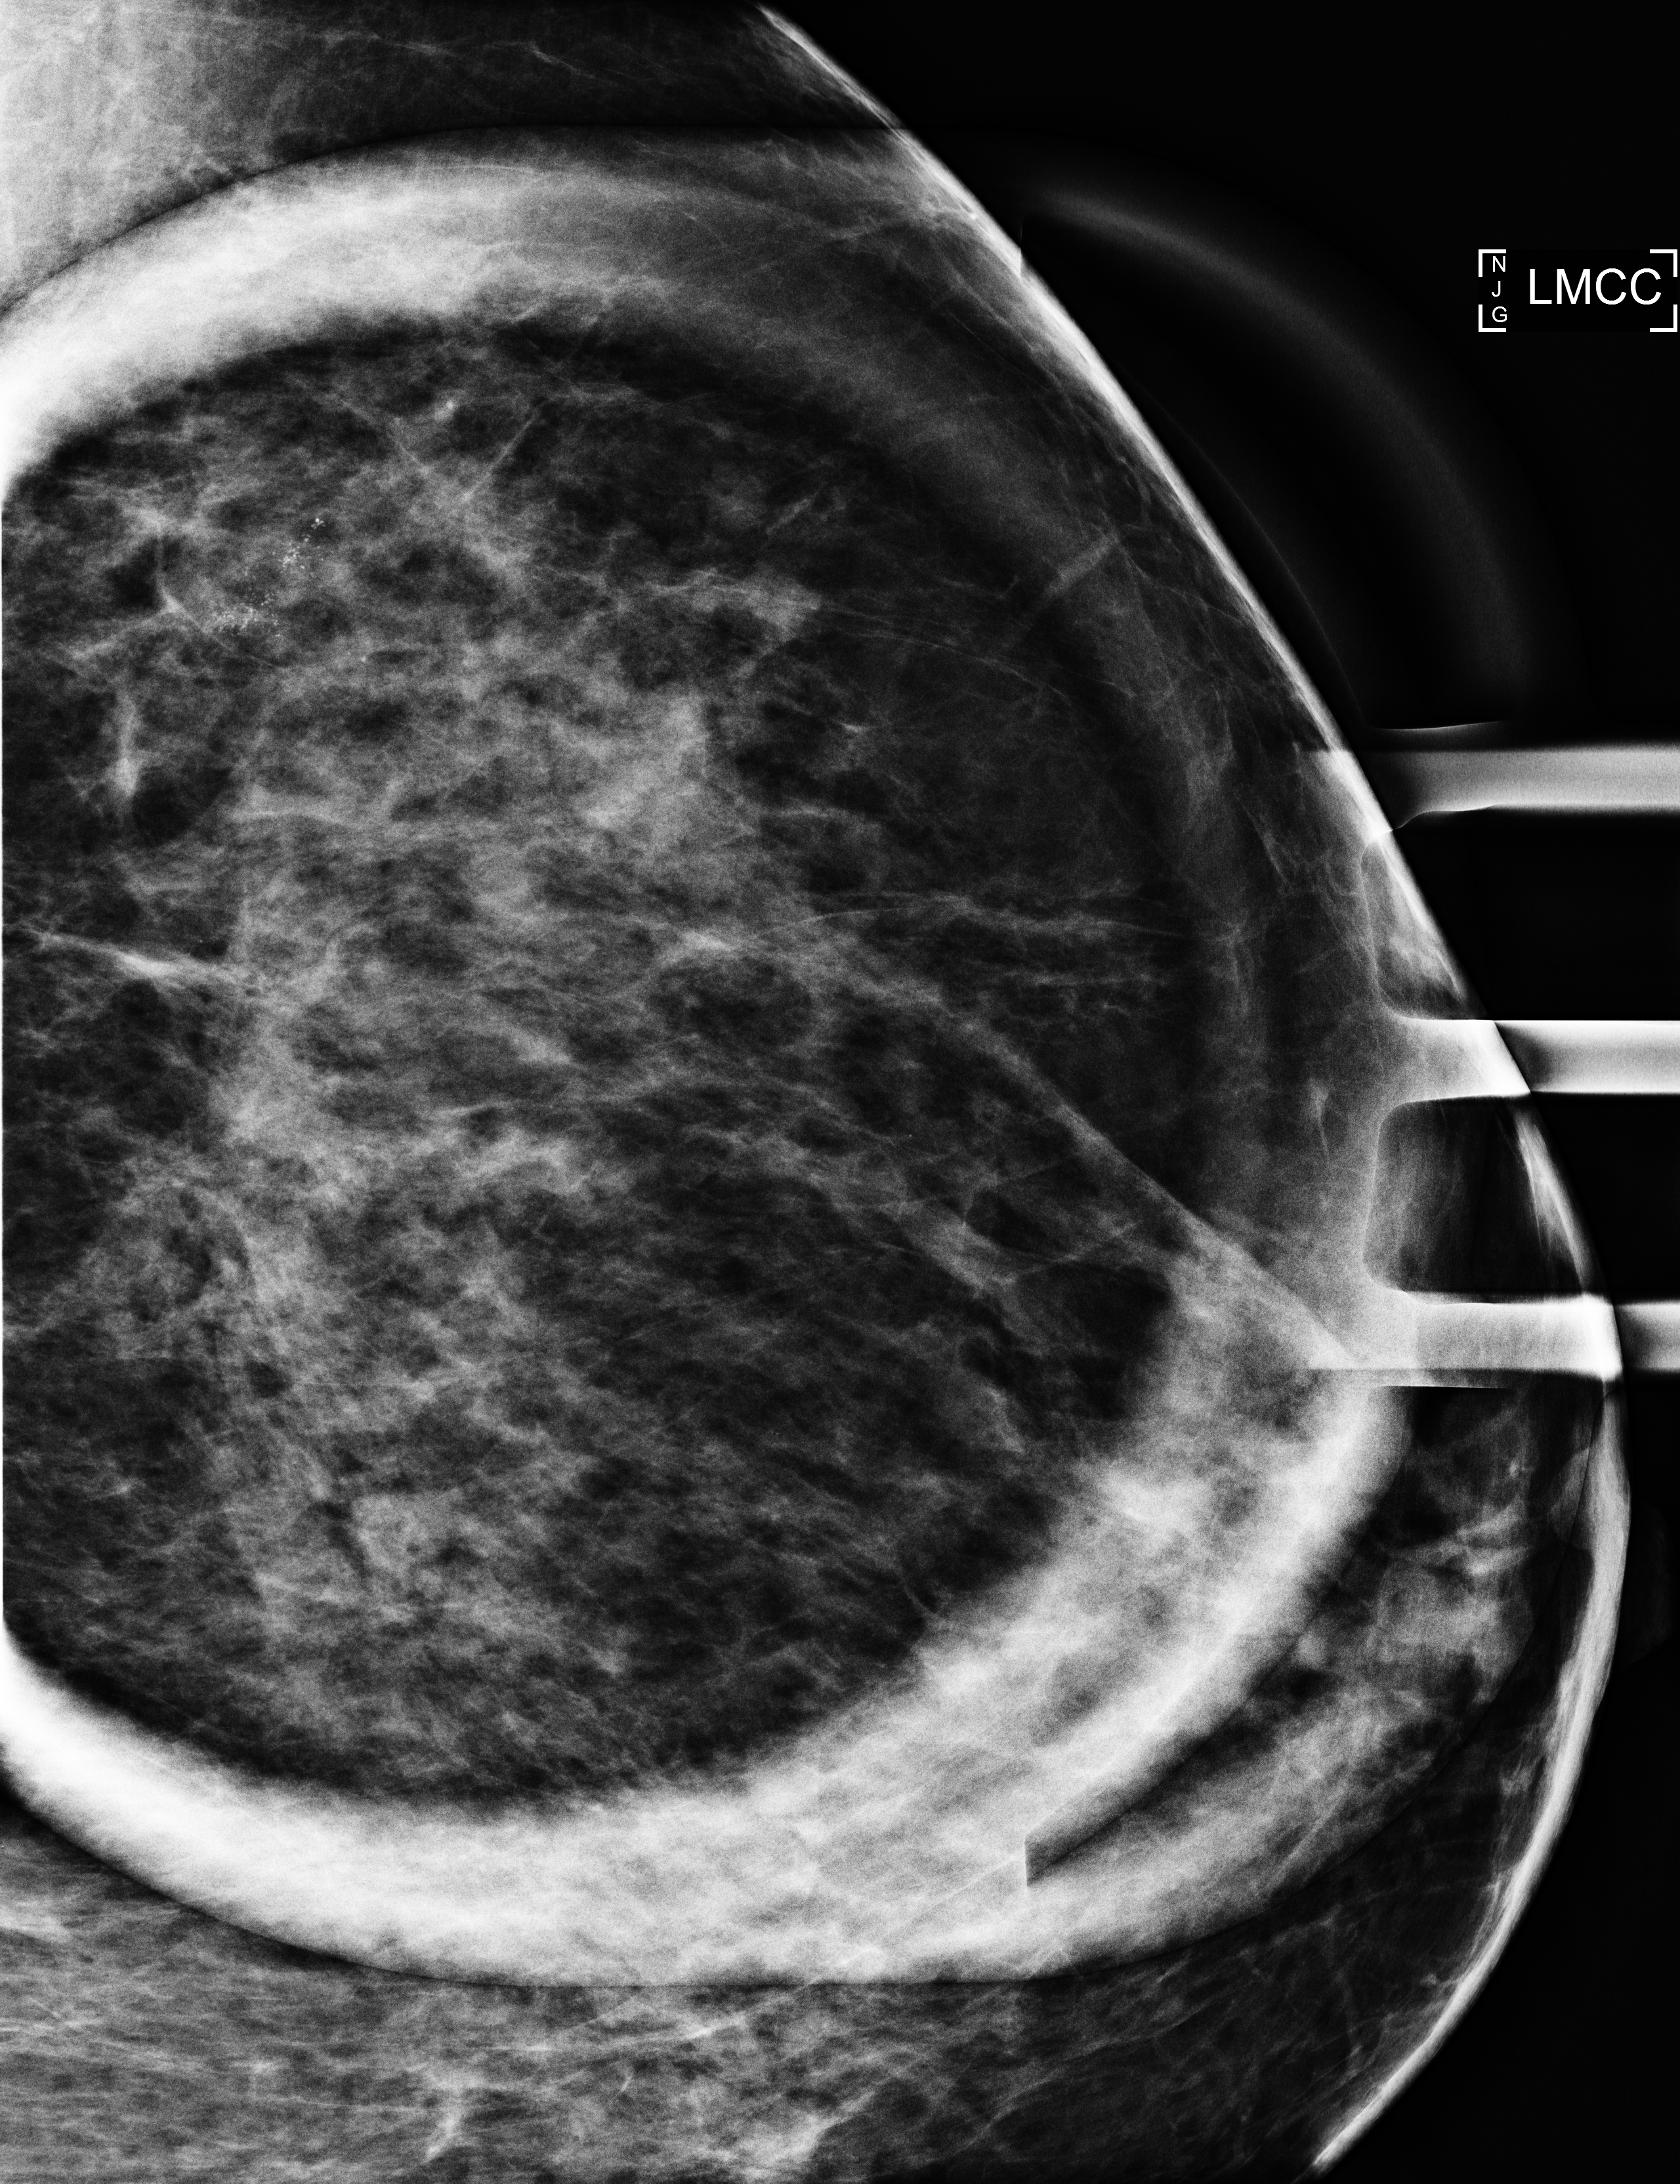
Additional (diagnostic) view; compressed breast thickness 49 mm. Patient aged 71 years (female).
Image type: full-field digital mammogram. Breast: left. Projection: CC view, magnification.